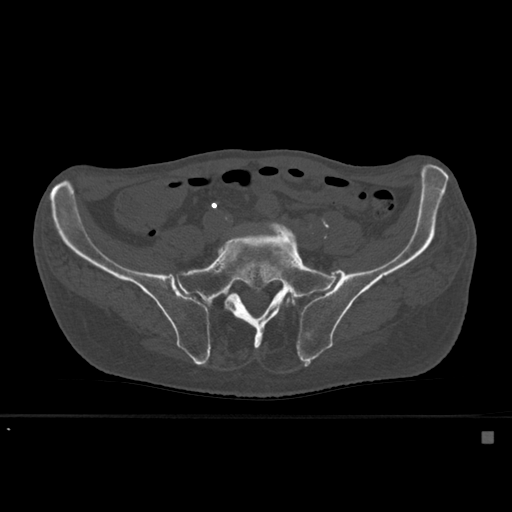
CT including the spine, one axial slice. Position 160 of 527 along the scan axis. Bone window (W 1800 / L 400 HU). 1.5 mm slice thickness. 512 × 512 image matrix. Patient: male, 78 years. Case-level facts recorded for this patient, not image findings: primary cancer: prostate.
Annotated regions visible in this slice (semi-automatic segmentation, software-assisted and operator-edited):
- L5 vertebra: box from (x=284, y=297) to (x=296, y=307) px